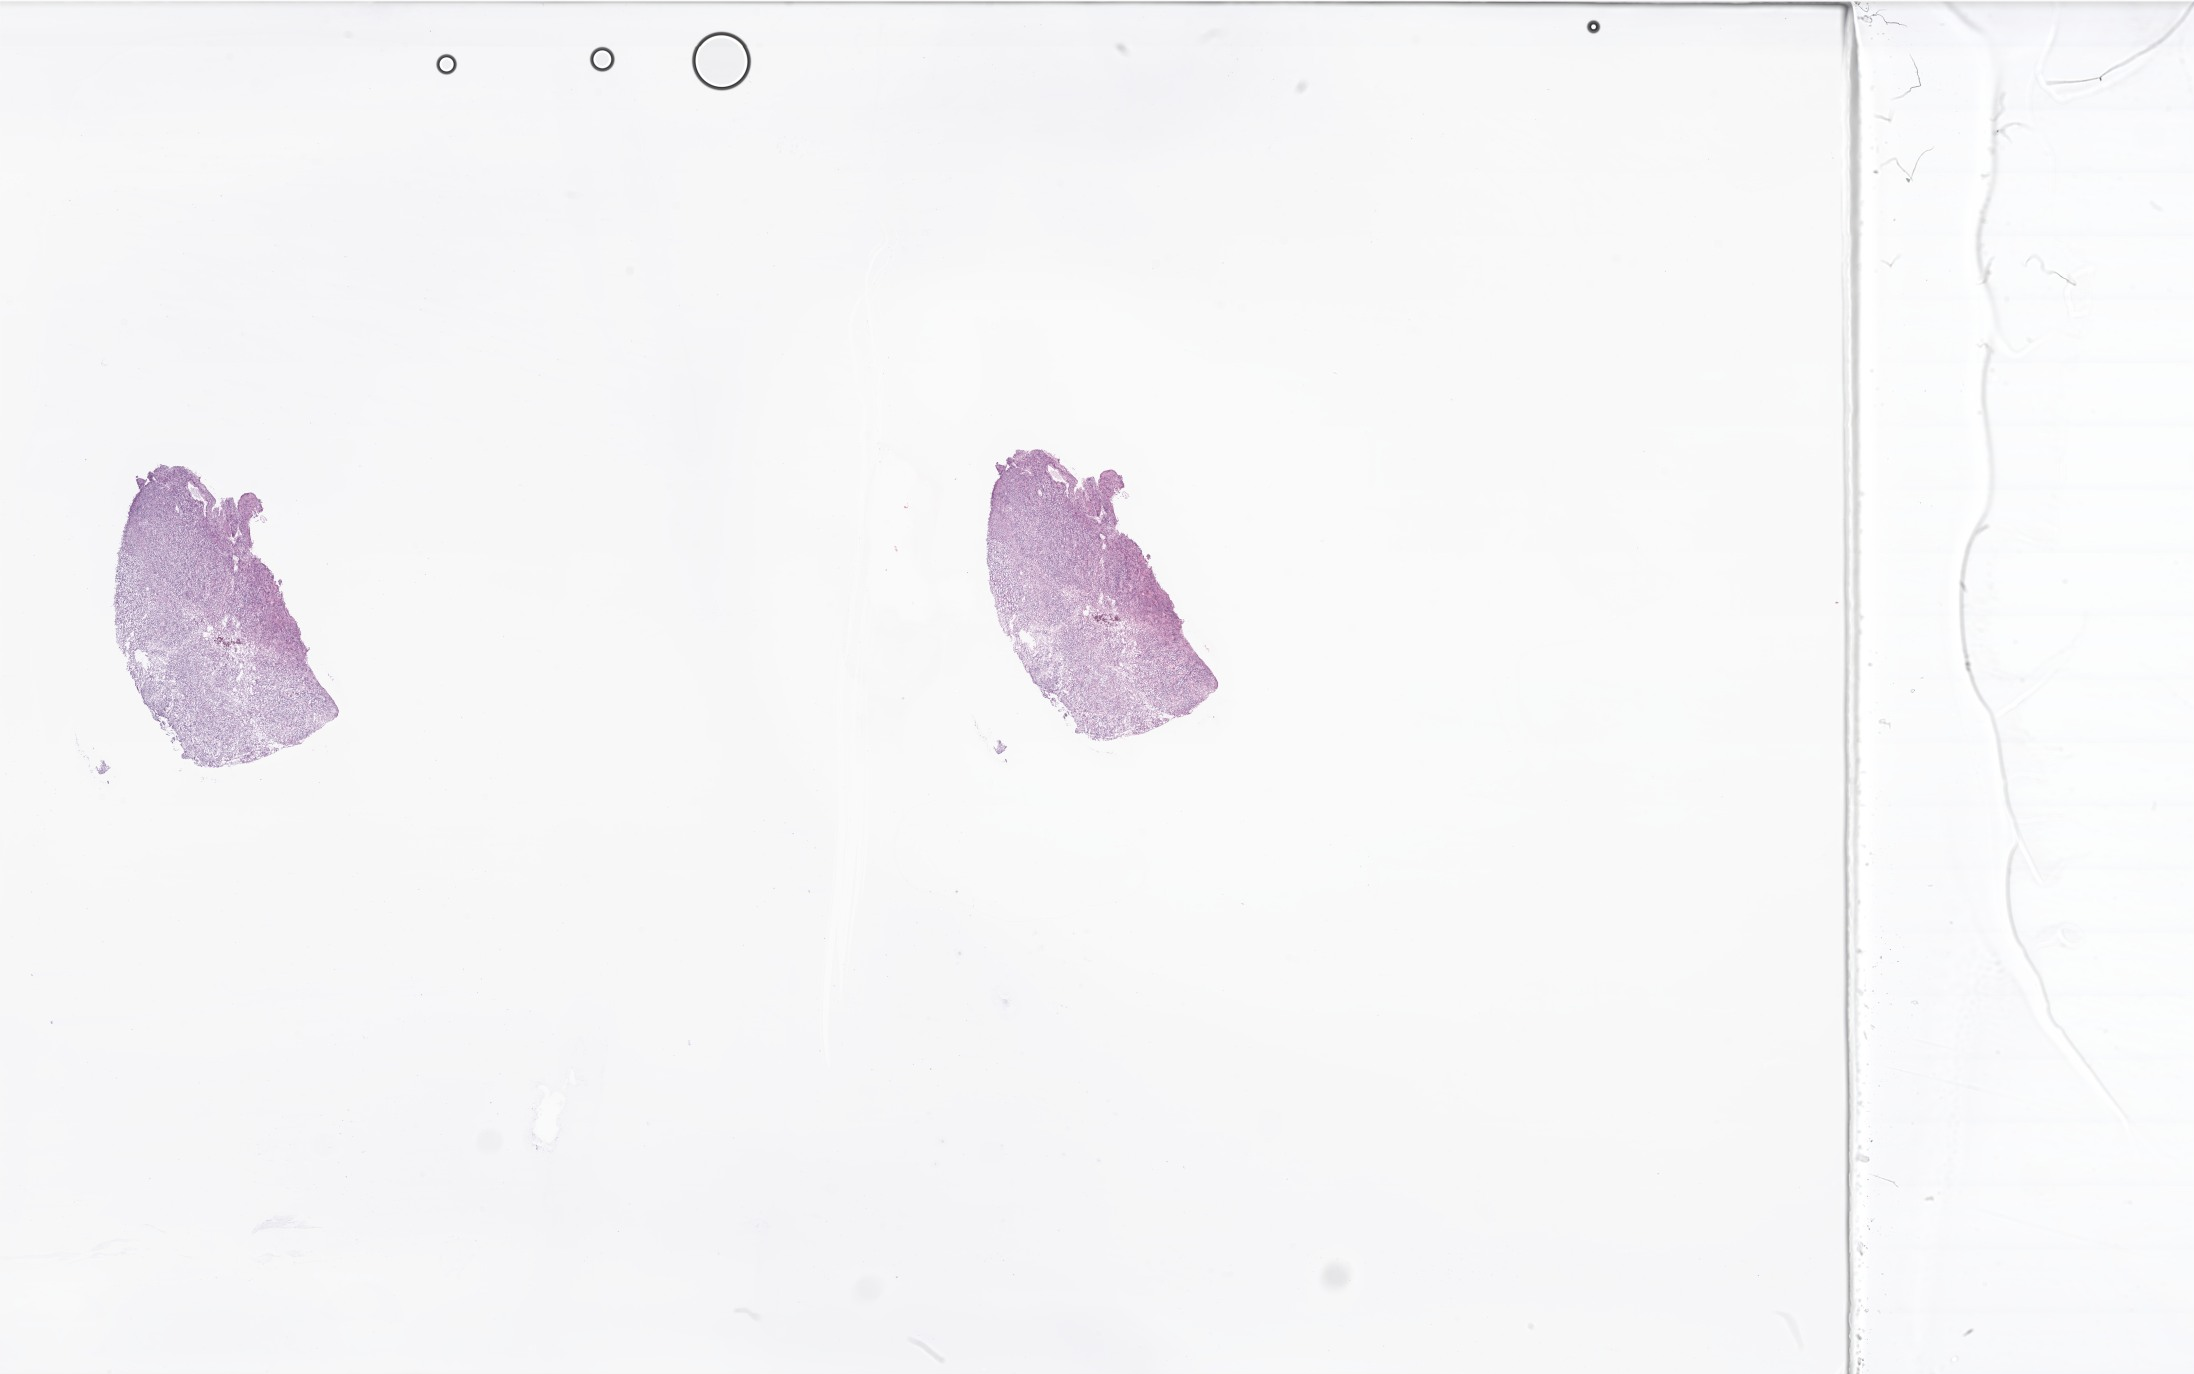
Whole-slide image, hematoxylin and eosin (H&E) stain of tumor tissue from the brain, shown as a low-resolution overview of the whole scanned area (about 37.0 x 23.2 mm). Frozen section (OCT-embedded). Patient female; age 252 days.
Recorded diagnosis: Ependymoma, NOS.